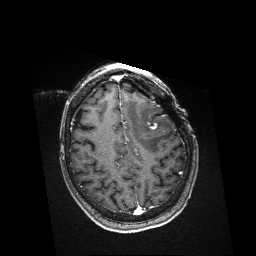
Brain MRI from a brain-tumour surgery series, one axial slice. Slice 125 of 176 in the series (ordered by position). T1-weighted post-contrast. 1 mm slice thickness. 256 × 256 image matrix. From the clinical record (not read from this slice): histopathology: Metastatic Melanoma; tumour location: Left Frontal.
Annotated regions visible in this slice (manually delineated by an expert):
- residual tumour: bounding box (x1, y1, x2, y2) in pixels: (148, 122, 158, 130)